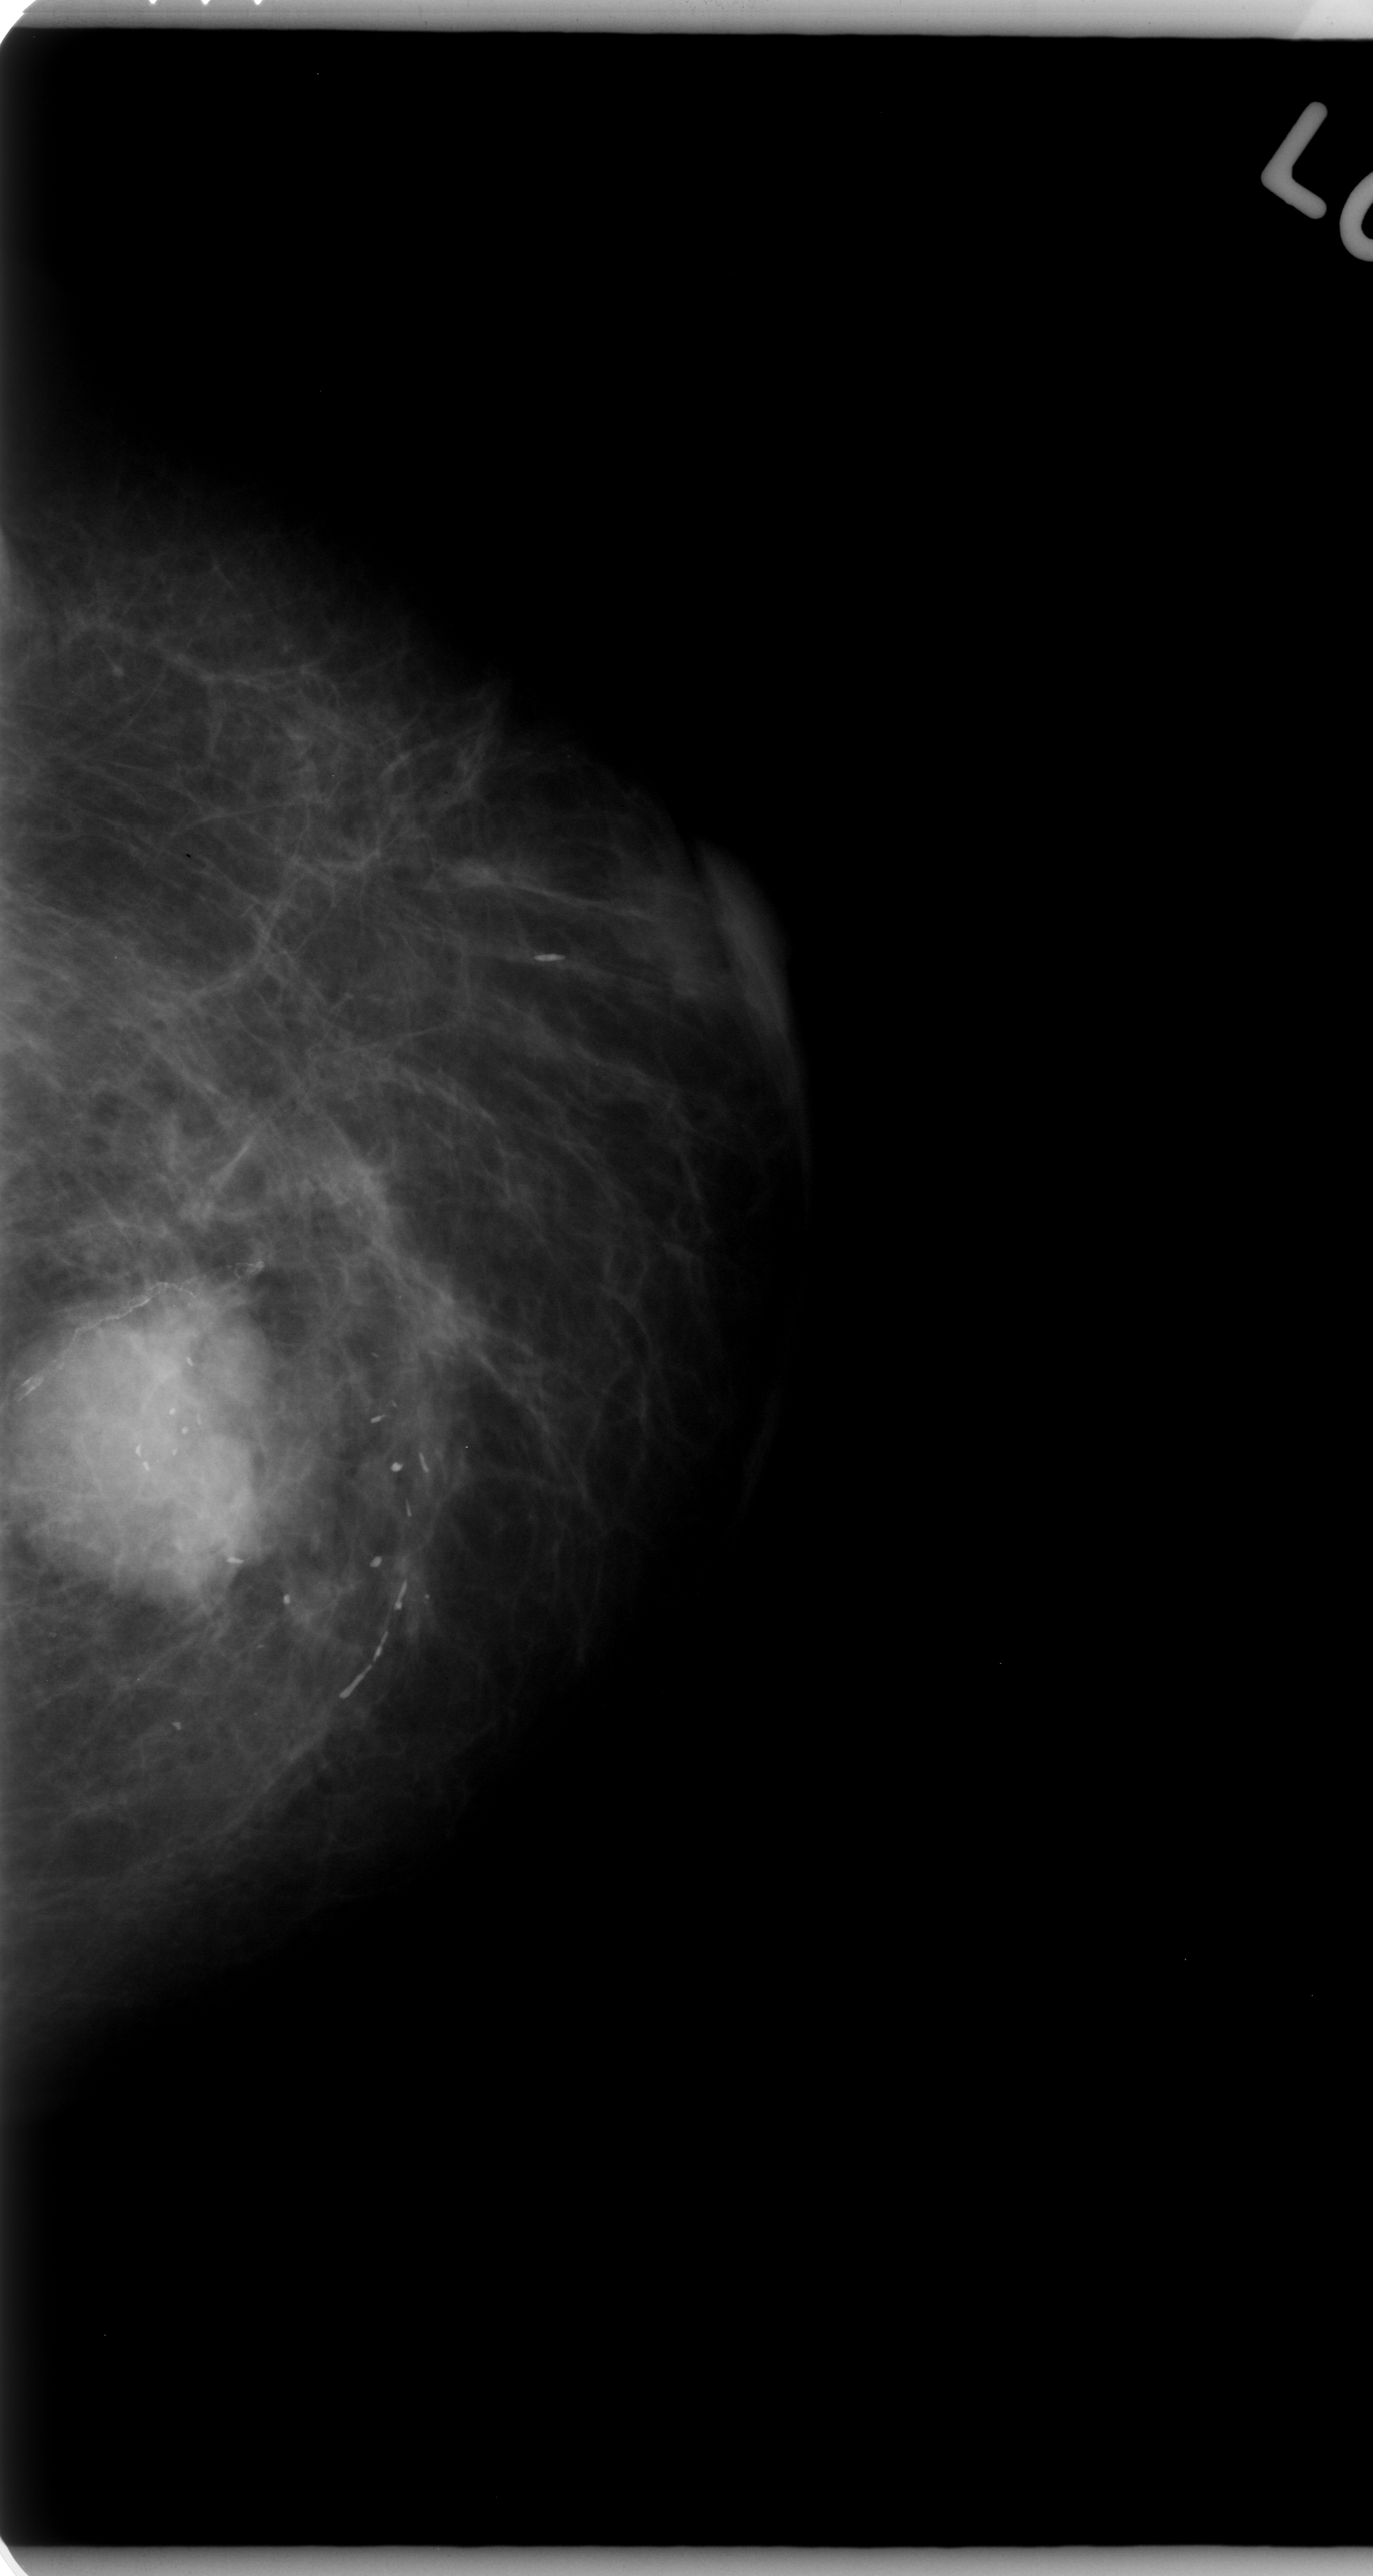
Scanned film-screen mammogram; left breast; craniocaudal (CC) view.
Abnormality record for this image: mass, shape lobulated, margins microlobulated; BI-RADS assessment category 5; pathology result (as recorded, not read from the image): malignant.